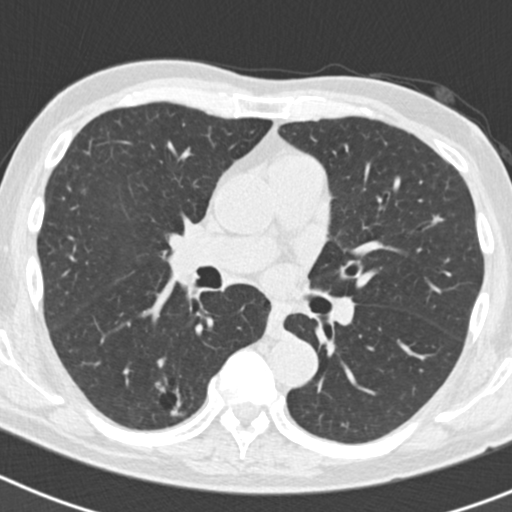
Axial slice from a low-dose chest CT screening exam, second annual screen, lung window (W 1500 / L -600 HU), 2 mm slice thickness. Male participant, aged 70 years at enrolment. Current smoker at enrolment.
- Lesion marked by an expert reader, box from (x=131, y=372) to (x=199, y=433) px.
- The screening reader recorded 5 non-calcified nodules or masses ≥4 mm on this exam; which of them this box marks is not recorded.
- Official screen result: positive, other.
- Participant outcome: lung cancer diagnosed 622 days after this screen (after the third annual screen) — bronchiolo-alveolar adenocarcinoma, NOS, right lower lobe, poorly differentiated (G3), stage IB (AJCC 6th edition), 30 mm at pathology.